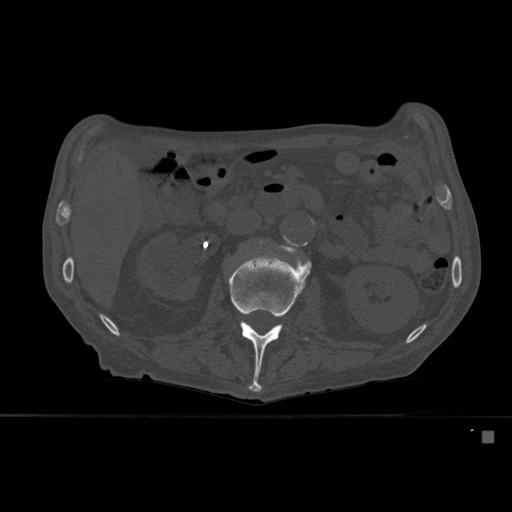
CT including the spine, one axial slice; slice 232 of 527 in the series (ordered by position); bone window (W 1800 / L 400 HU); 512 × 512 image matrix, field of view 373 × 373 mm. Male patient, age 78 years. From the clinical record (not read from this slice): primary cancer: prostate.
Annotated regions visible in this slice (semi-automatic segmentation, software-assisted and operator-edited):
- L2 vertebra: box from (x=228, y=257) to (x=312, y=392) px
- L3 vertebra: (x=279, y=236)–(x=308, y=257)